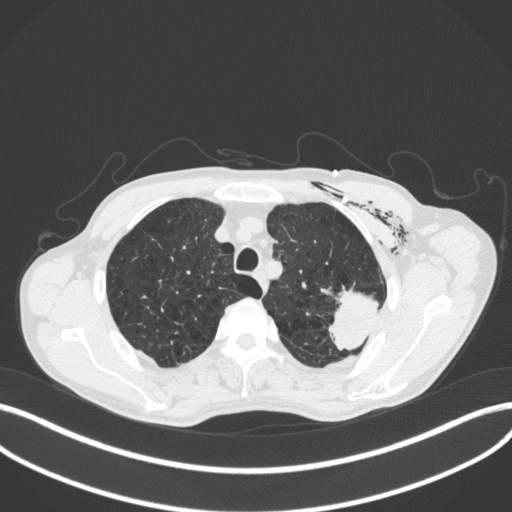
Chest CT, one axial slice; position 332 of 416 along the scan axis; reconstruction kernel B31f; 120 kVp; lung window (W 1500 / L -600 HU); 512 × 512 image matrix. Male patient, age 58 years. From the clinical record (not read from this slice): clinical TNM (as recorded): T3 N0 M0.
Structures marked on this image (rectangle marked by the reading radiologist):
- lung tumour (recorded histology: adenocarcinoma): bounding box <317,283,381,352> (left, top, right, bottom; pixels)